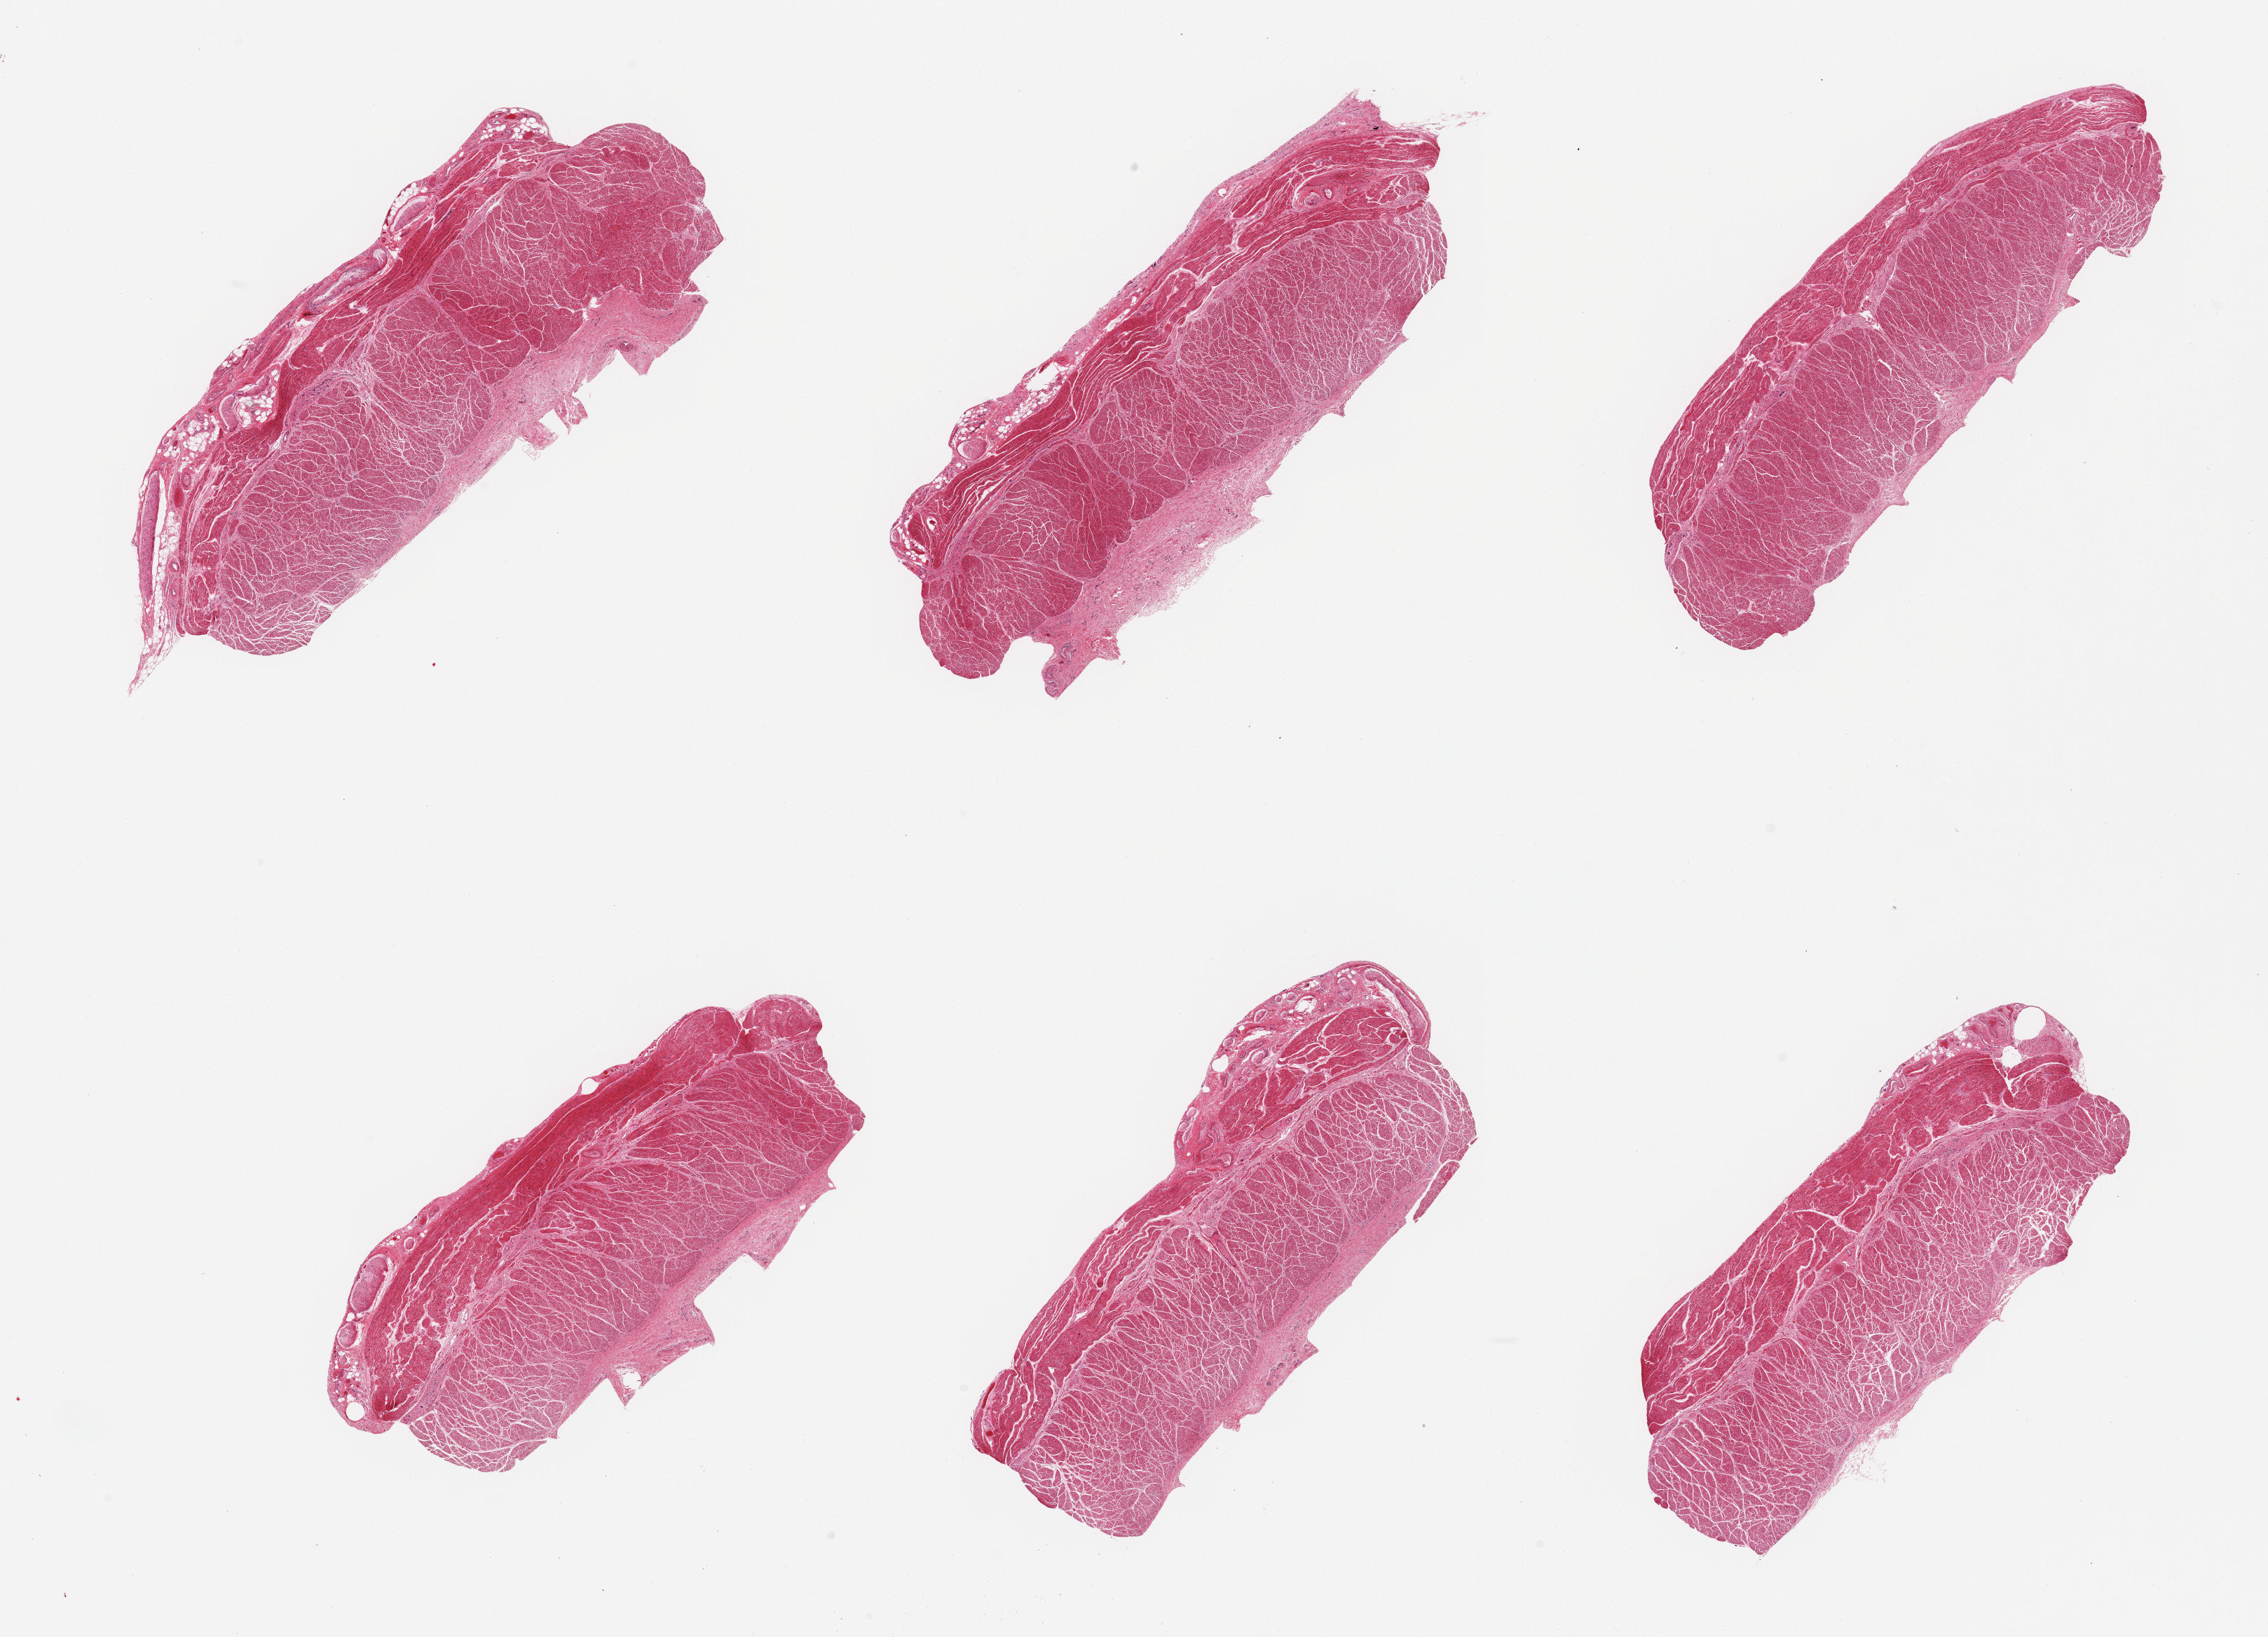
H&E whole-slide image, whole scanned area (about 25.6 x 18.5 mm, slide scanned at 20x) shown as a low-resolution overview, PAXgene-fixed, paraffin-embedded tissue, section of gastroesophageal junction (target tissue), donor tissue sample. Female donor.
* review note (as recorded): 6 pieces, attached nerve